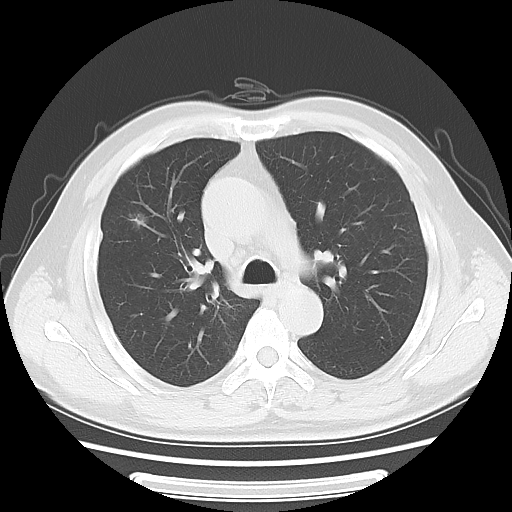
Chest CT, one axial slice; slice 40 of 63 in the series (ordered by position); reconstruction kernel LUNG; 120 kVp; lung window (W 1500 / L -600 HU); 5 mm slice thickness; 512 × 512 image matrix, field of view 360 × 360 mm. Male patient, age 63 years. Case-level facts recorded for this patient, not image findings: clinical TNM (as recorded): T1c N0 M0.
Outlined on this slice (bounding box drawn by a radiologist):
- lung tumour (recorded histology: adenocarcinoma): bounding box (x1, y1, x2, y2) in pixels: (124, 204, 148, 231)